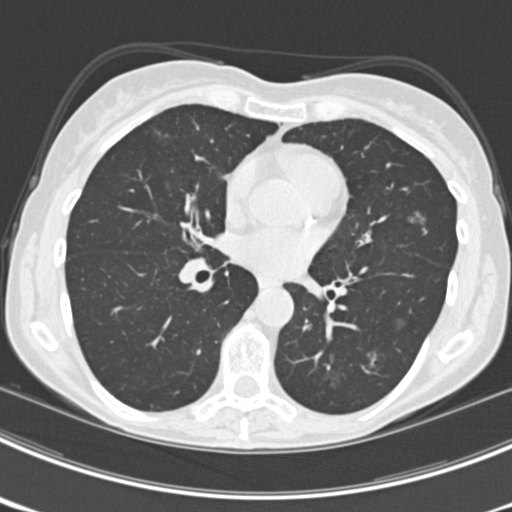
Low-dose screening chest CT, axial slice, third screening round (two years after baseline), lung window (W 1500 / L -600 HU), 2 mm slice thickness, standard (soft-tissue) reconstruction kernel (B30f), slice 105 of 225 in the series. Female participant, aged 63 years at enrolment. Current smoker at enrolment.
Lesion marked by an expert reader, box from (x=404, y=200) to (x=441, y=236) px. The screening reader recorded 9 non-calcified nodules or masses ≥4 mm on this exam (left upper lobe, right upper lobe, left upper lobe, left lower lobe, right middle lobe, left lower lobe, left lower lobe, right lower lobe, right lower lobe); which of them this box marks is not recorded. Later outcome: lung cancer diagnosed 15 days after this screen — bronchiolo-alveolar adenocarcinoma, NOS, right upper lobe, right middle lobe, right lower lobe, left upper lobe, left lower lobe, moderately differentiated (G2), stage IV (AJCC 6th edition).